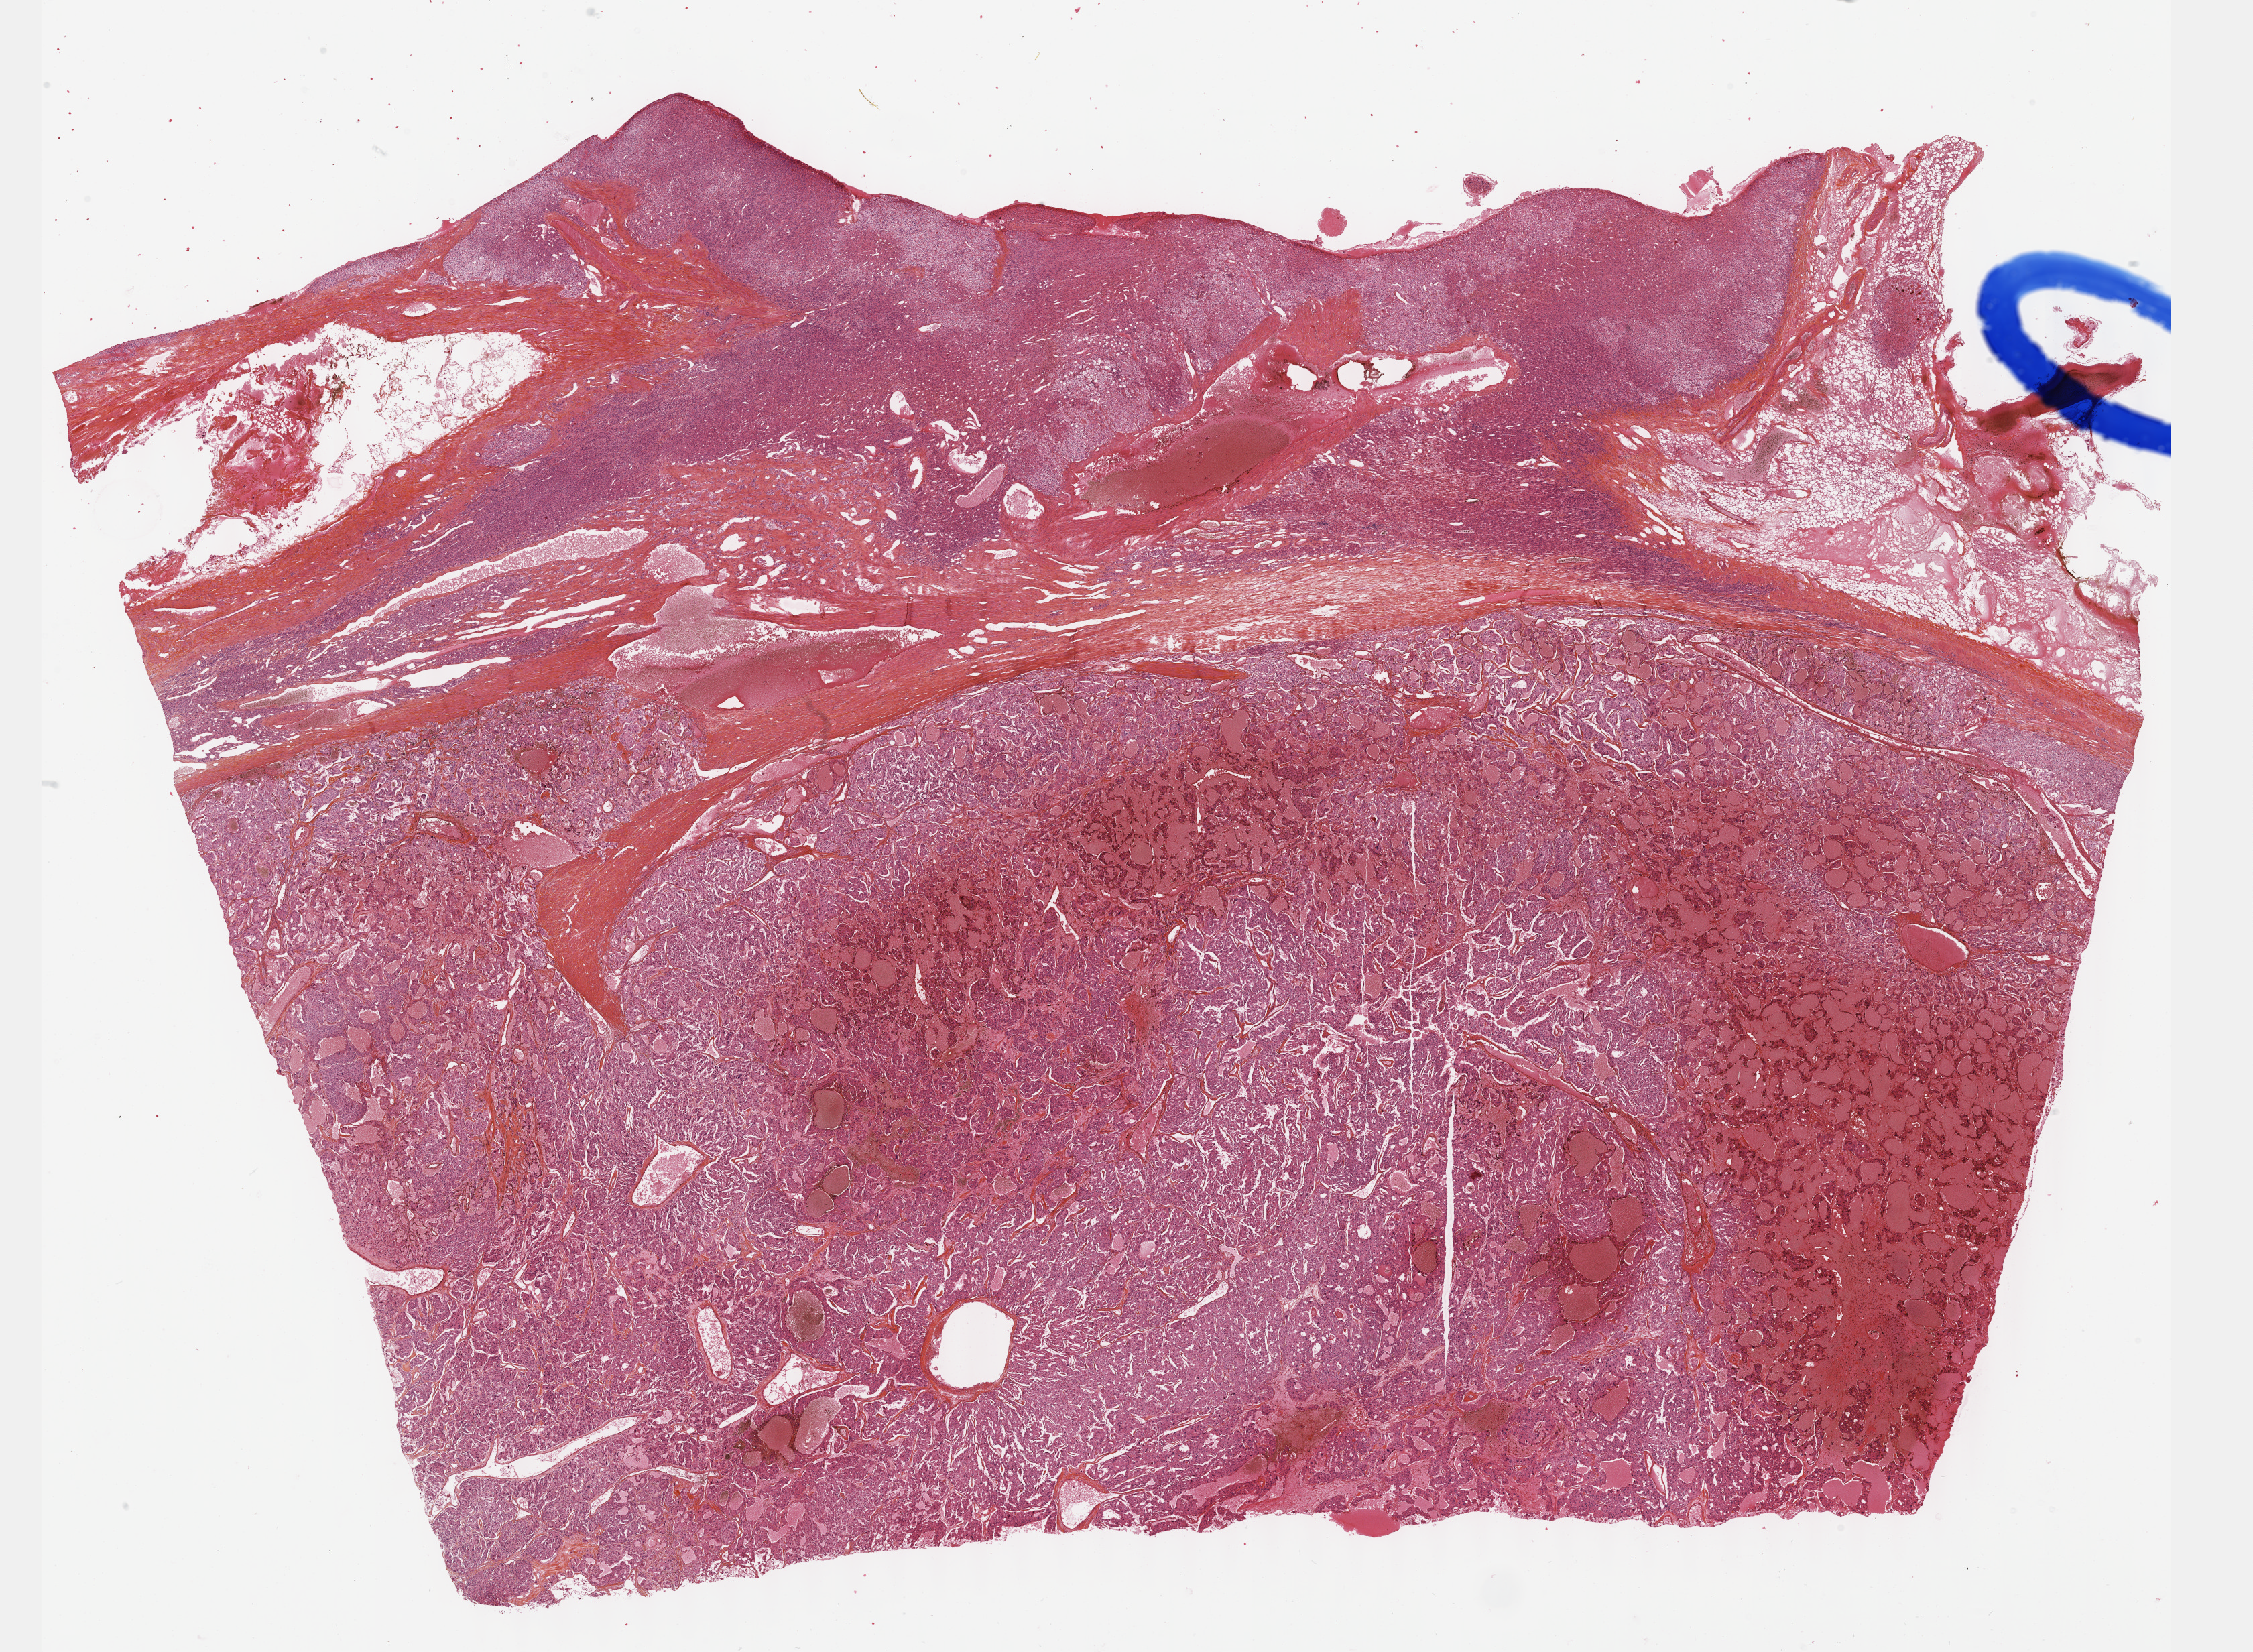
Whole-slide histology image, Hematoxylin and eosin (H&E) stained — a low-resolution overview of the entire scanned area, about 27.2 x 19.9 mm; formalin-fixed paraffin-embedded (FFPE) diagnostic section; primary tumour sample from the adrenal gland. Male patient; age at initial diagnosis 40 years.
- lymph nodes positive (case pathology): 0 of 1 examined
- pathologic diagnosis: Pheochromocytoma, malignant